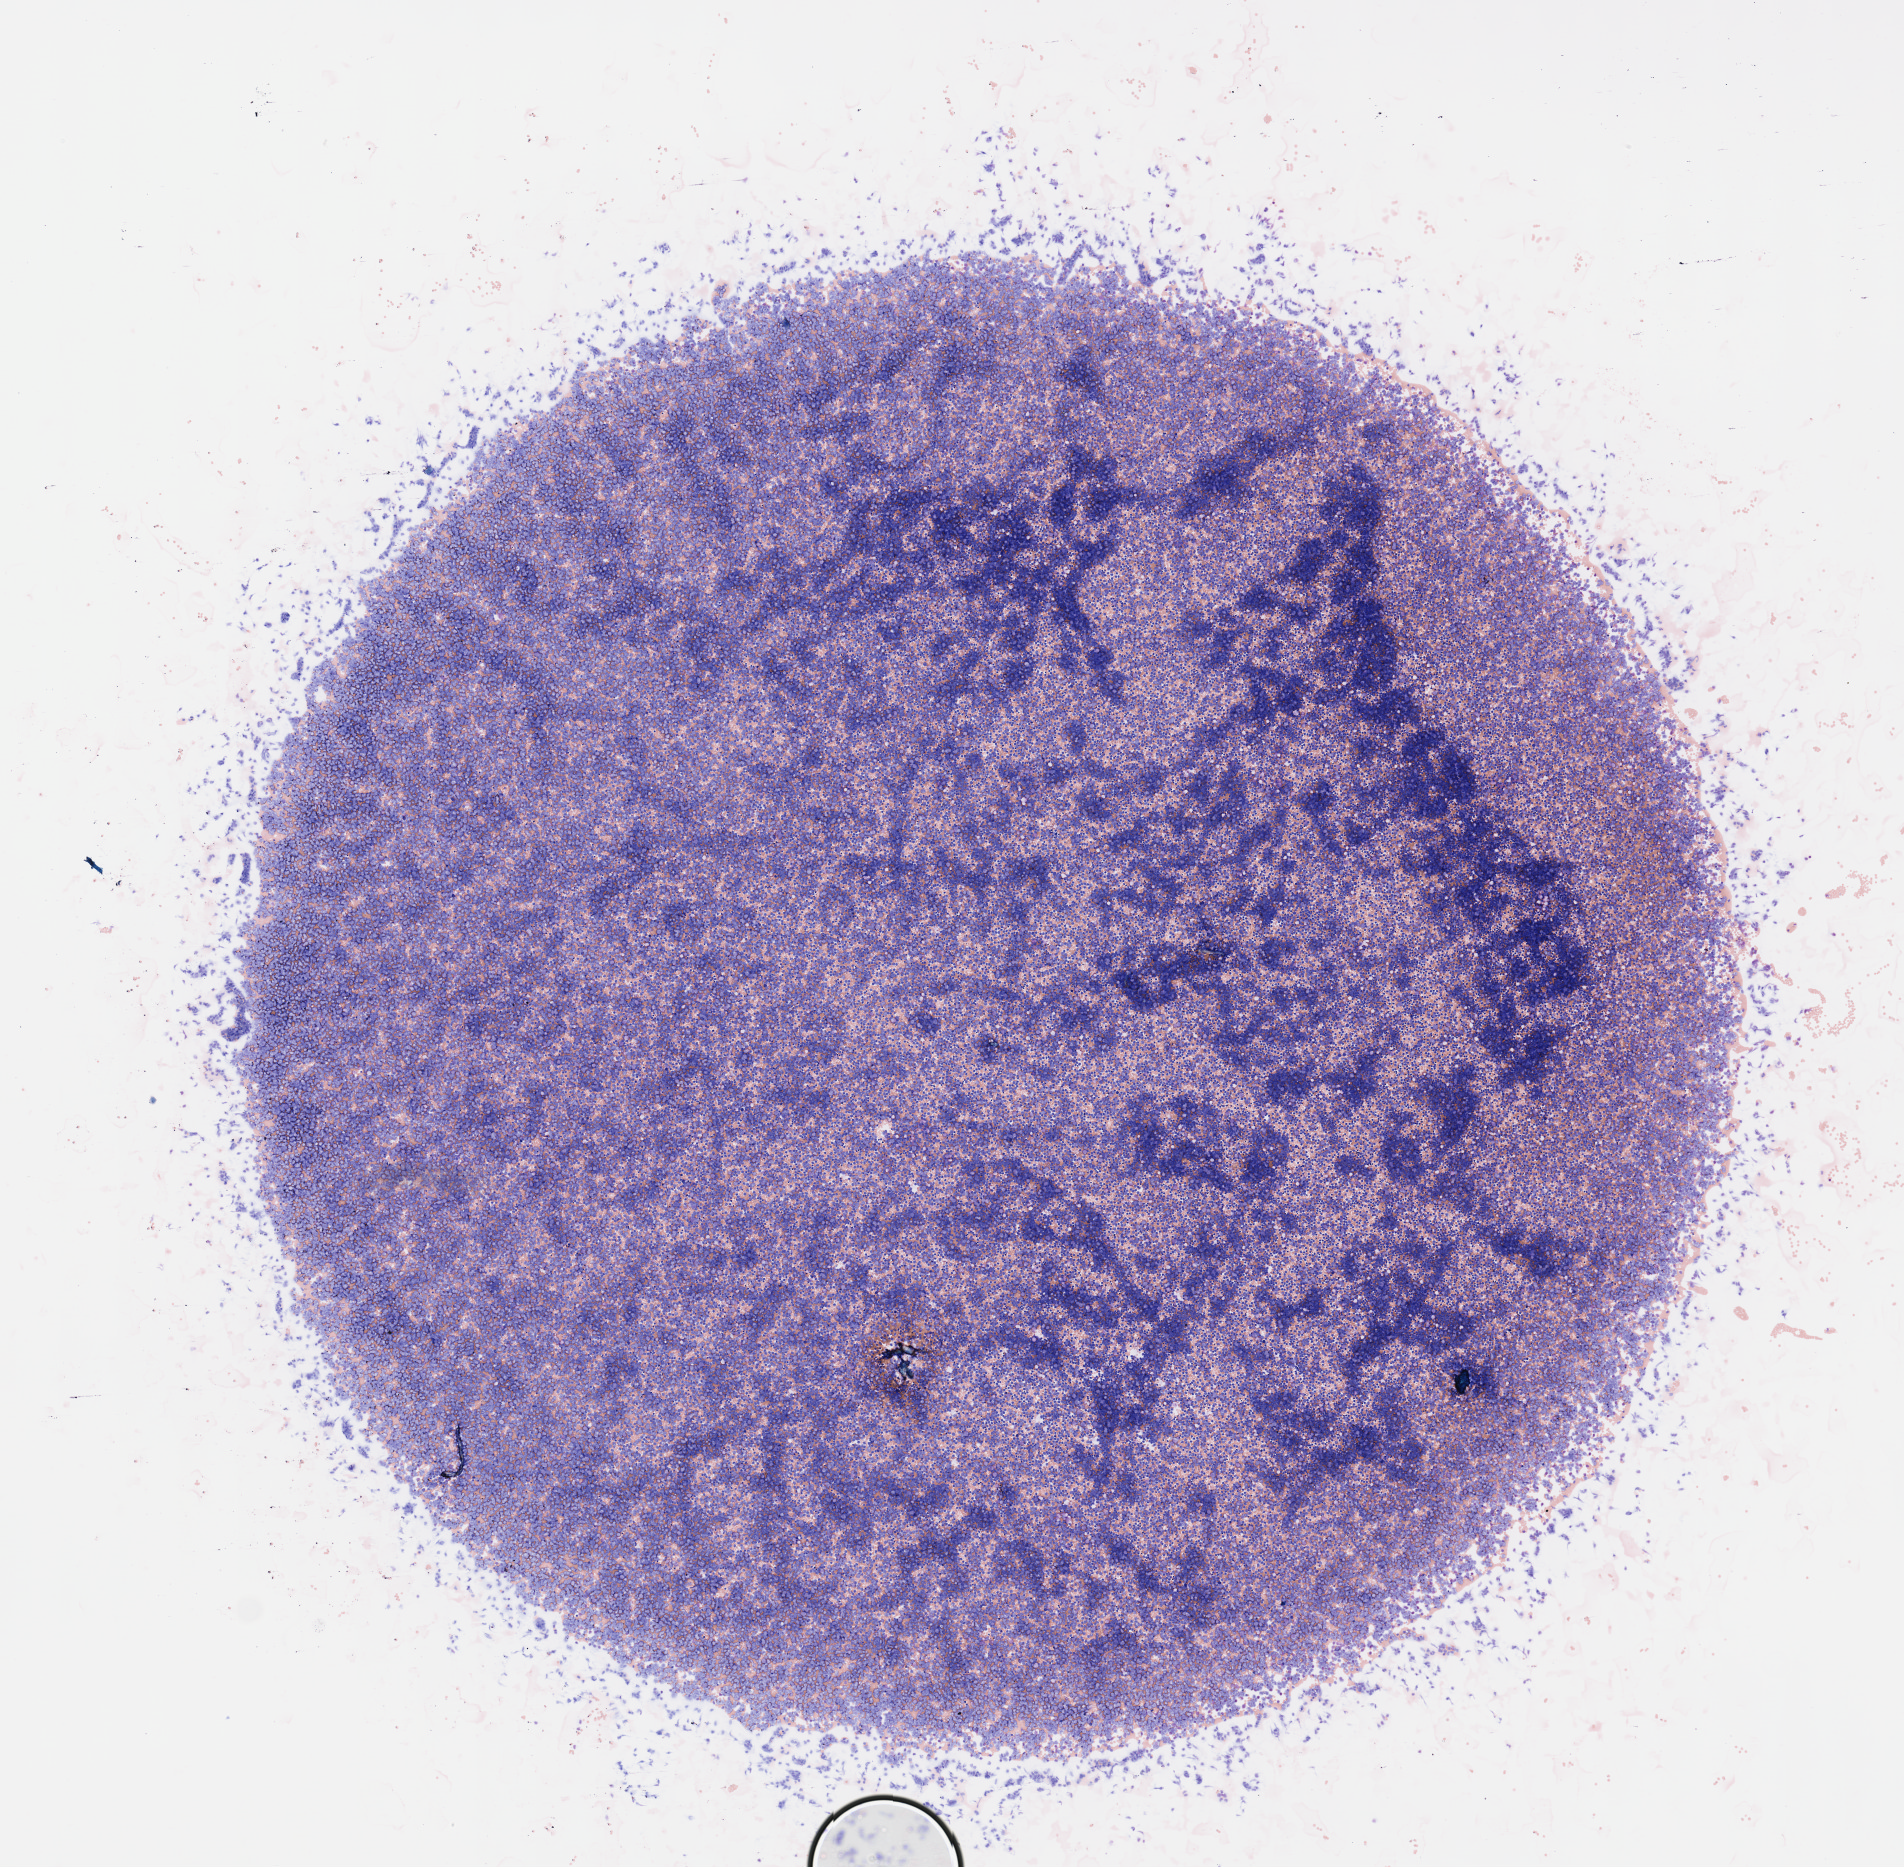
Whole-slide histology image, H&E-stained, a low-resolution overview of the entire scanned area, about 7.5 x 7.4 mm (slide scanned at 40x); peripheral blood (leukaemic) sample. Patient: male, age 60 years. Blasts: 20%.
Diagnosis: Acute Myeloid Leukemia. WHO classification: AML not otherwise specified.